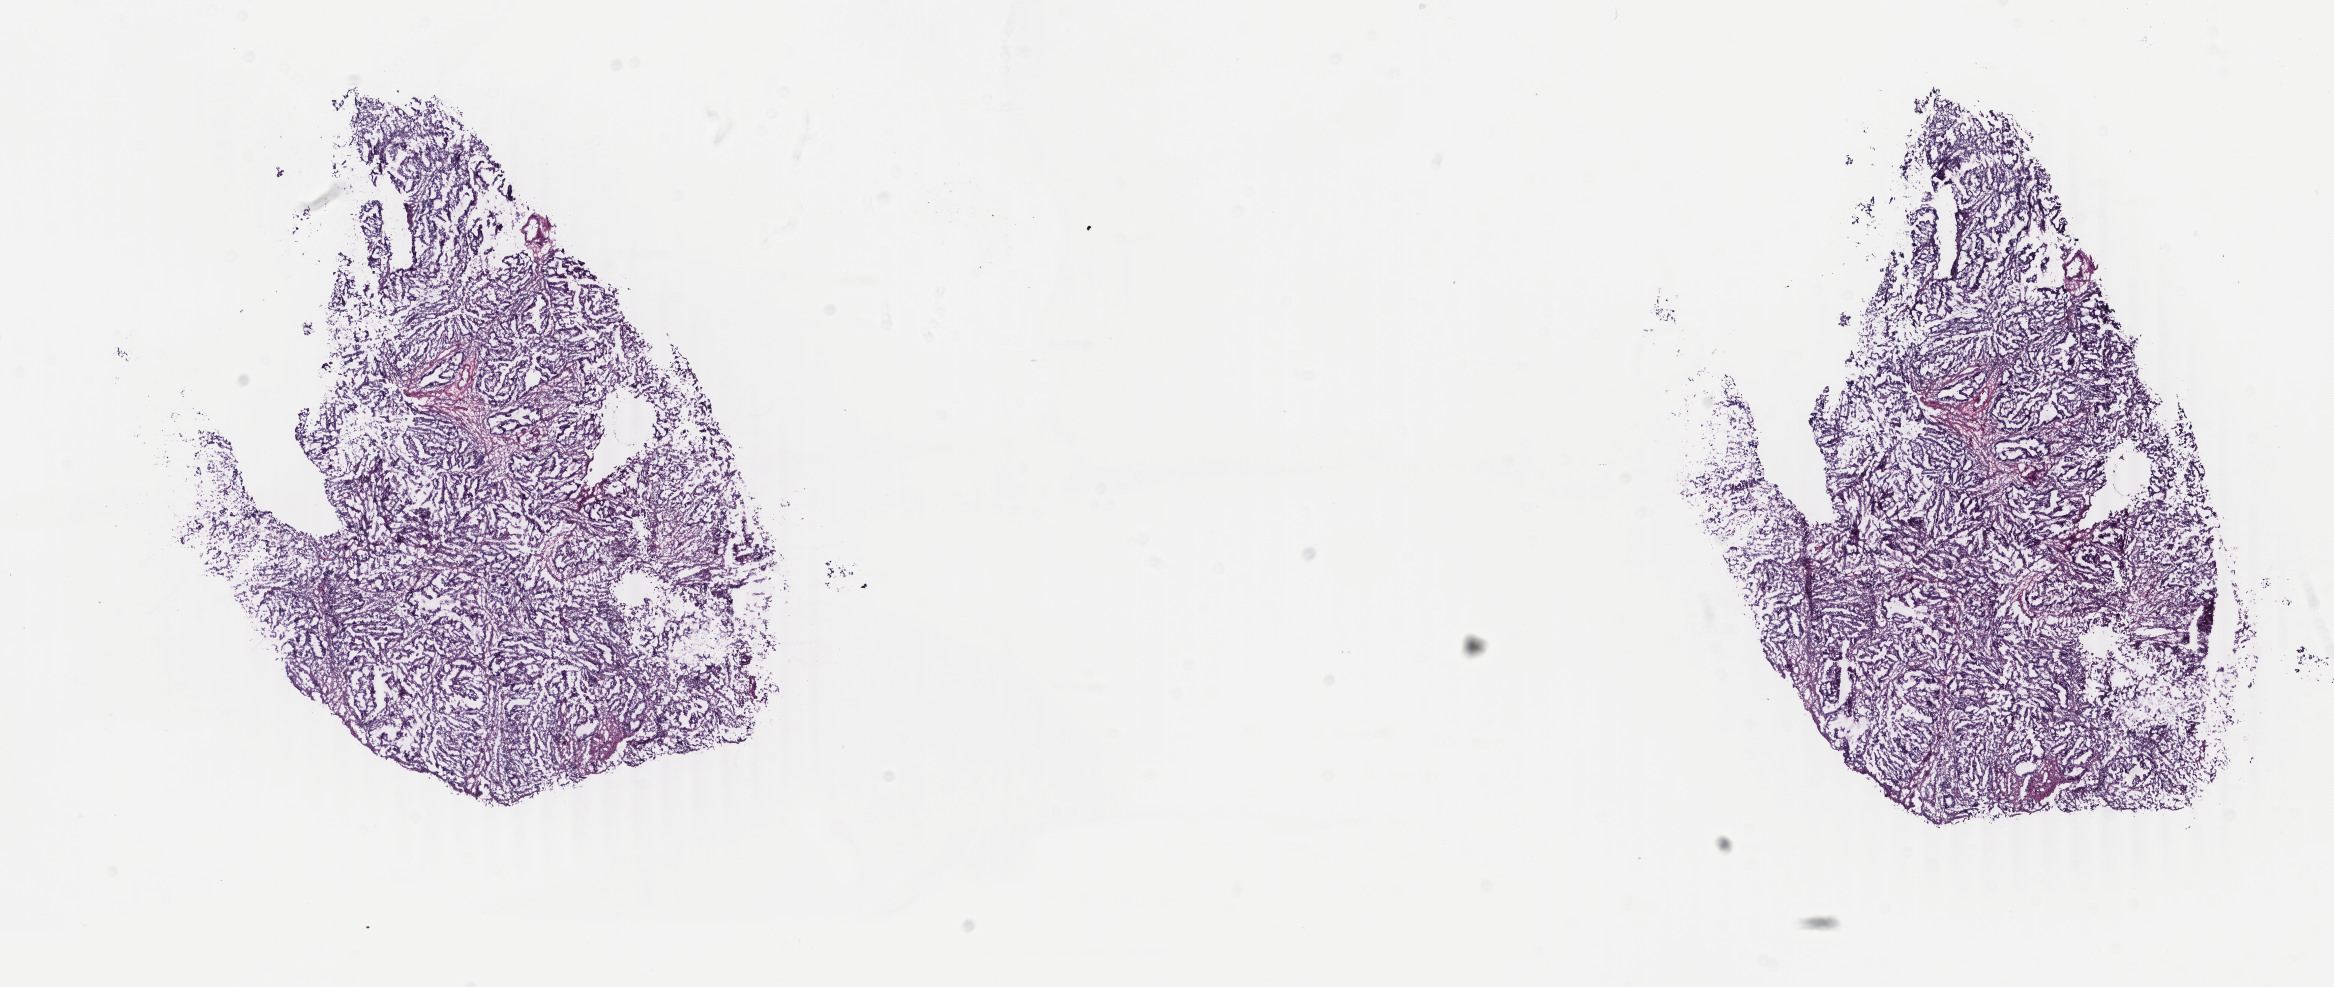
H&E-stained whole-slide image — low-resolution overview of the scanned area, about 18.6 x 7.8 mm, frozen section from the top of the tissue portion, primary tumour sample from the uterus. Female patient; age at initial diagnosis 81 years. Histologic grade: G2 (moderately differentiated). Slide review estimates, as recorded: tumour cells 75%, tumour nuclei 75%, normal cells 0%, stromal cells 20%, necrosis 5%. Inflammatory infiltration, as recorded: lymphocyte infiltration 30%, monocyte infiltration 20%, neutrophil infiltration 30%.
* FIGO stage: IB
* diagnosis: Endometrioid adenocarcinoma, NOS (endometrium)